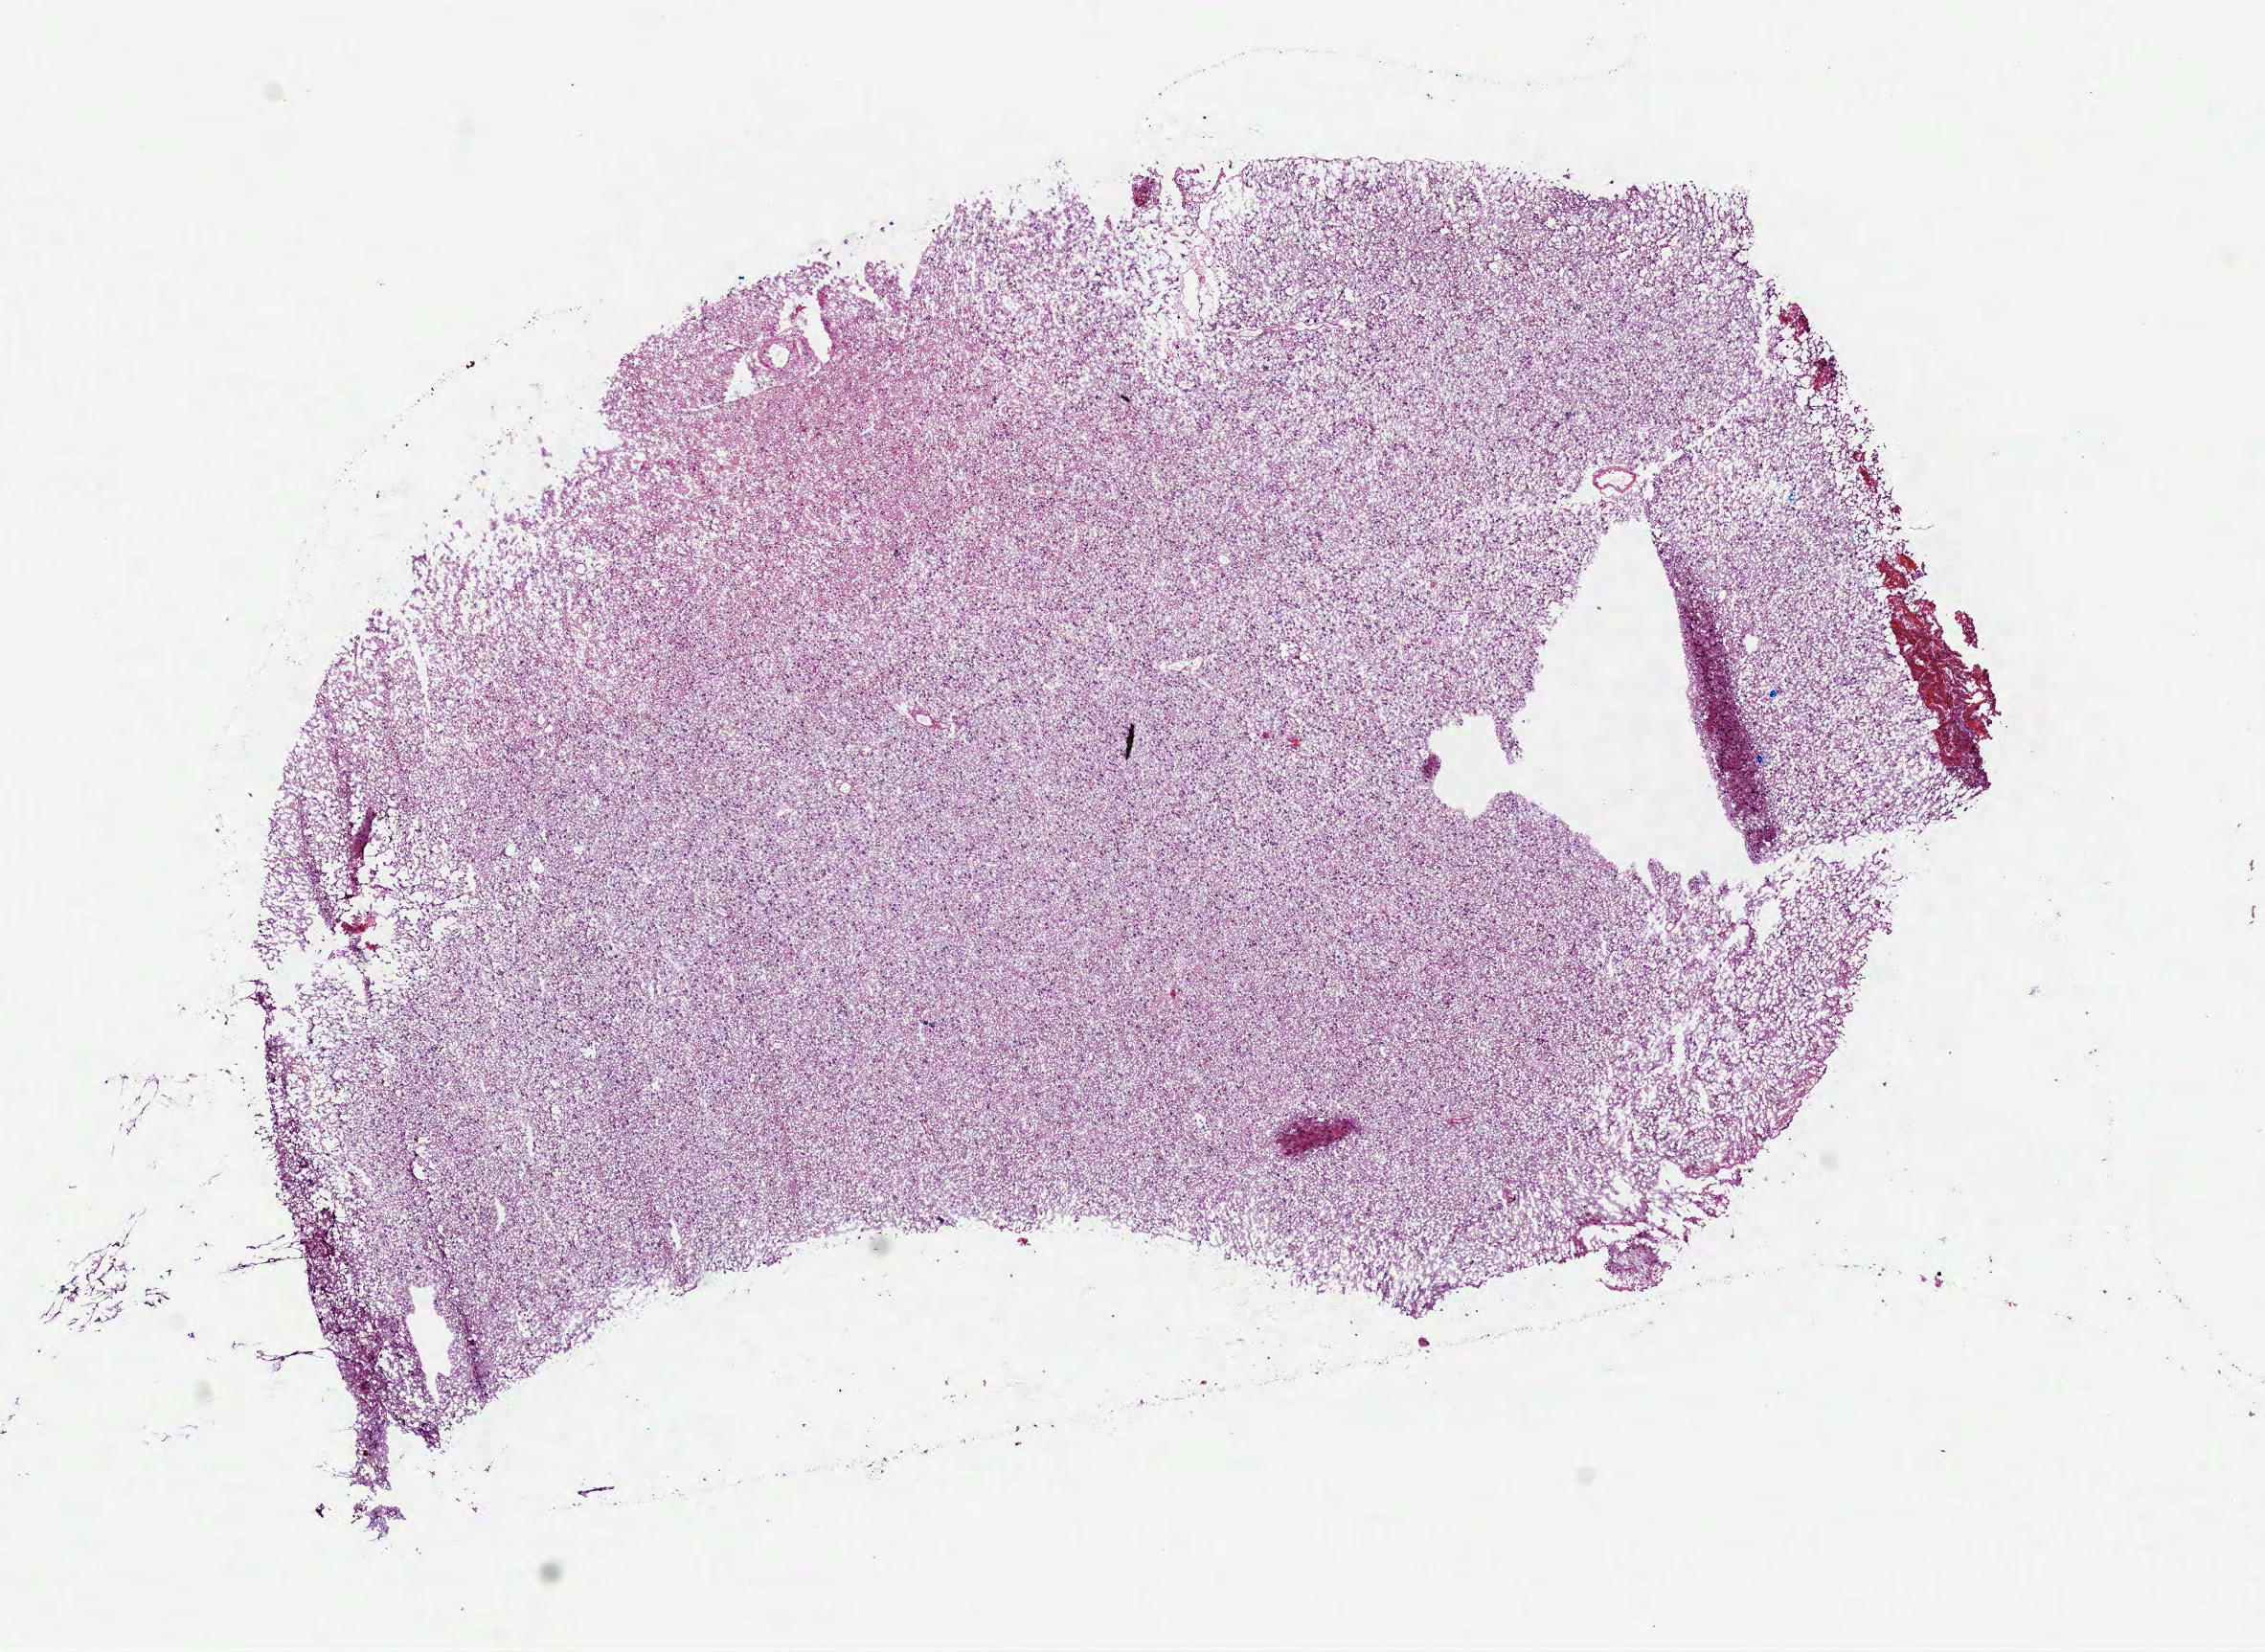
Digitized Hematoxylin and eosin (H&E) stained tissue section (whole slide) — a low-resolution overview of the entire scanned area, about 9.5 x 7.0 mm (slide scanned at 40x); frozen section from the bottom of the tissue portion; sample: recurrent tumour, brain. Female, age 48 years at initial diagnosis. Pathologist review of this section (percent, as recorded): tumour cells 100%, tumour nuclei 60%, normal cells 0%, stromal cells 0%, necrosis 0%.
This section: recurrent tumour. Patient diagnosis: Glioblastoma.